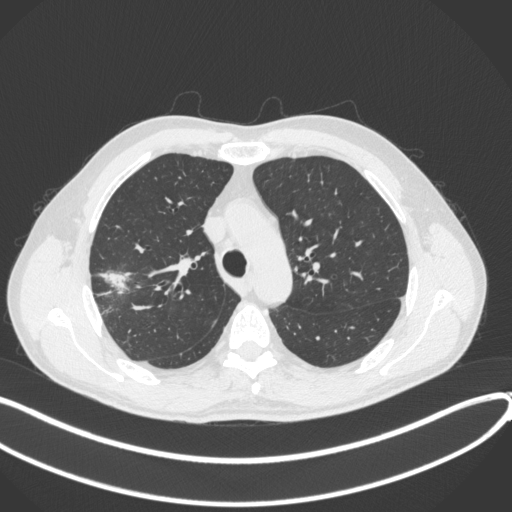
Chest CT, one axial slice. Position 303 of 381 along the scan axis. Reconstruction kernel B31f. Lung window (W 1500 / L -600 HU). 1 mm slice thickness. 512 × 512 image matrix, field of view 400 × 400 mm. Patient: male, 62 years. From the clinical record (not read from this slice): clinical TNM (as recorded): T1c N0 M0.
Annotated regions visible in this slice (rectangle marked by the reading radiologist):
- lung tumour (recorded histology: adenocarcinoma): bounding box <97,267,135,297> (left, top, right, bottom; pixels)